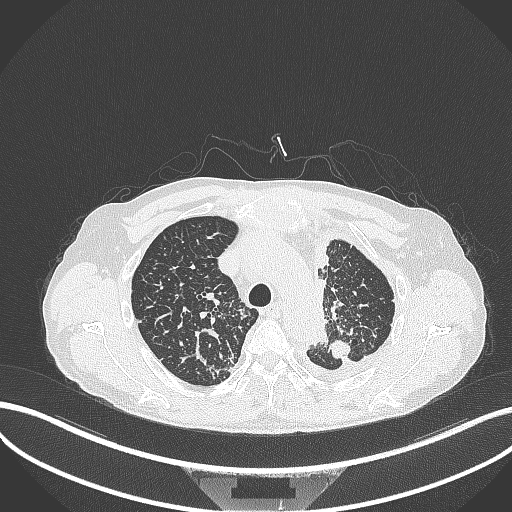
Chest CT, one axial slice. Slice 271 of 325 in the series (ordered by position). 120 kVp. Lung window (W 1500 / L -600 HU). 1 mm slice thickness. 512 × 512 image matrix, field of view 400 × 400 mm. Patient: male, 58 years. Case-level facts recorded for this patient, not image findings: clinical TNM (as recorded): T1c N3 M1.
Structures marked on this image (bounding box drawn by a radiologist):
- lung tumour (recorded histology: adenocarcinoma): bounding box <326,338,352,361> (left, top, right, bottom; pixels)